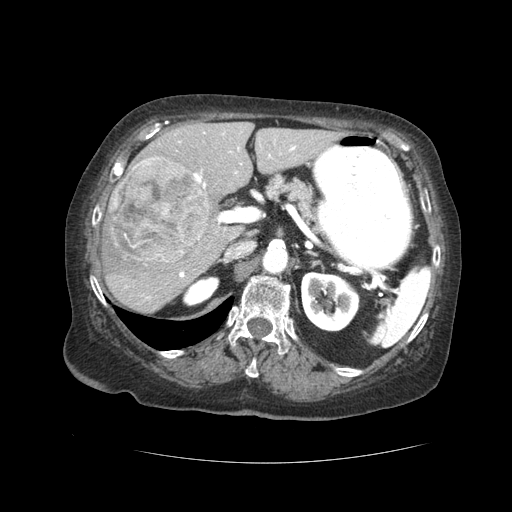
Contrast-enhanced abdominal CT (liver protocol), one axial slice; slice 21 of 59 in the series (ordered by position); 120 kVp; soft-tissue window (W 400 / L 40 HU); 2.5 mm slice thickness; 512 × 512 image matrix, field of view 380 × 380 mm. From the clinical record (not read from this slice): diagnosis: hepatocellular carcinoma (patient treated with transarterial chemoembolisation; whether this scan precedes or follows treatment is not stated here); TNM stage (as recorded): Stage-I; Child-Pugh class: A.
Annotated regions visible in this slice (semi-automatically segmented with operator editing):
- liver parenchyma outside the tumour (the mass and vessels are separate outlines, so this box may not span the whole liver): bounding box (x1, y1, x2, y2) in pixels: (102, 122, 340, 312)
- mass: (105, 155, 209, 265)
- liver vessels: (126, 132, 296, 299)